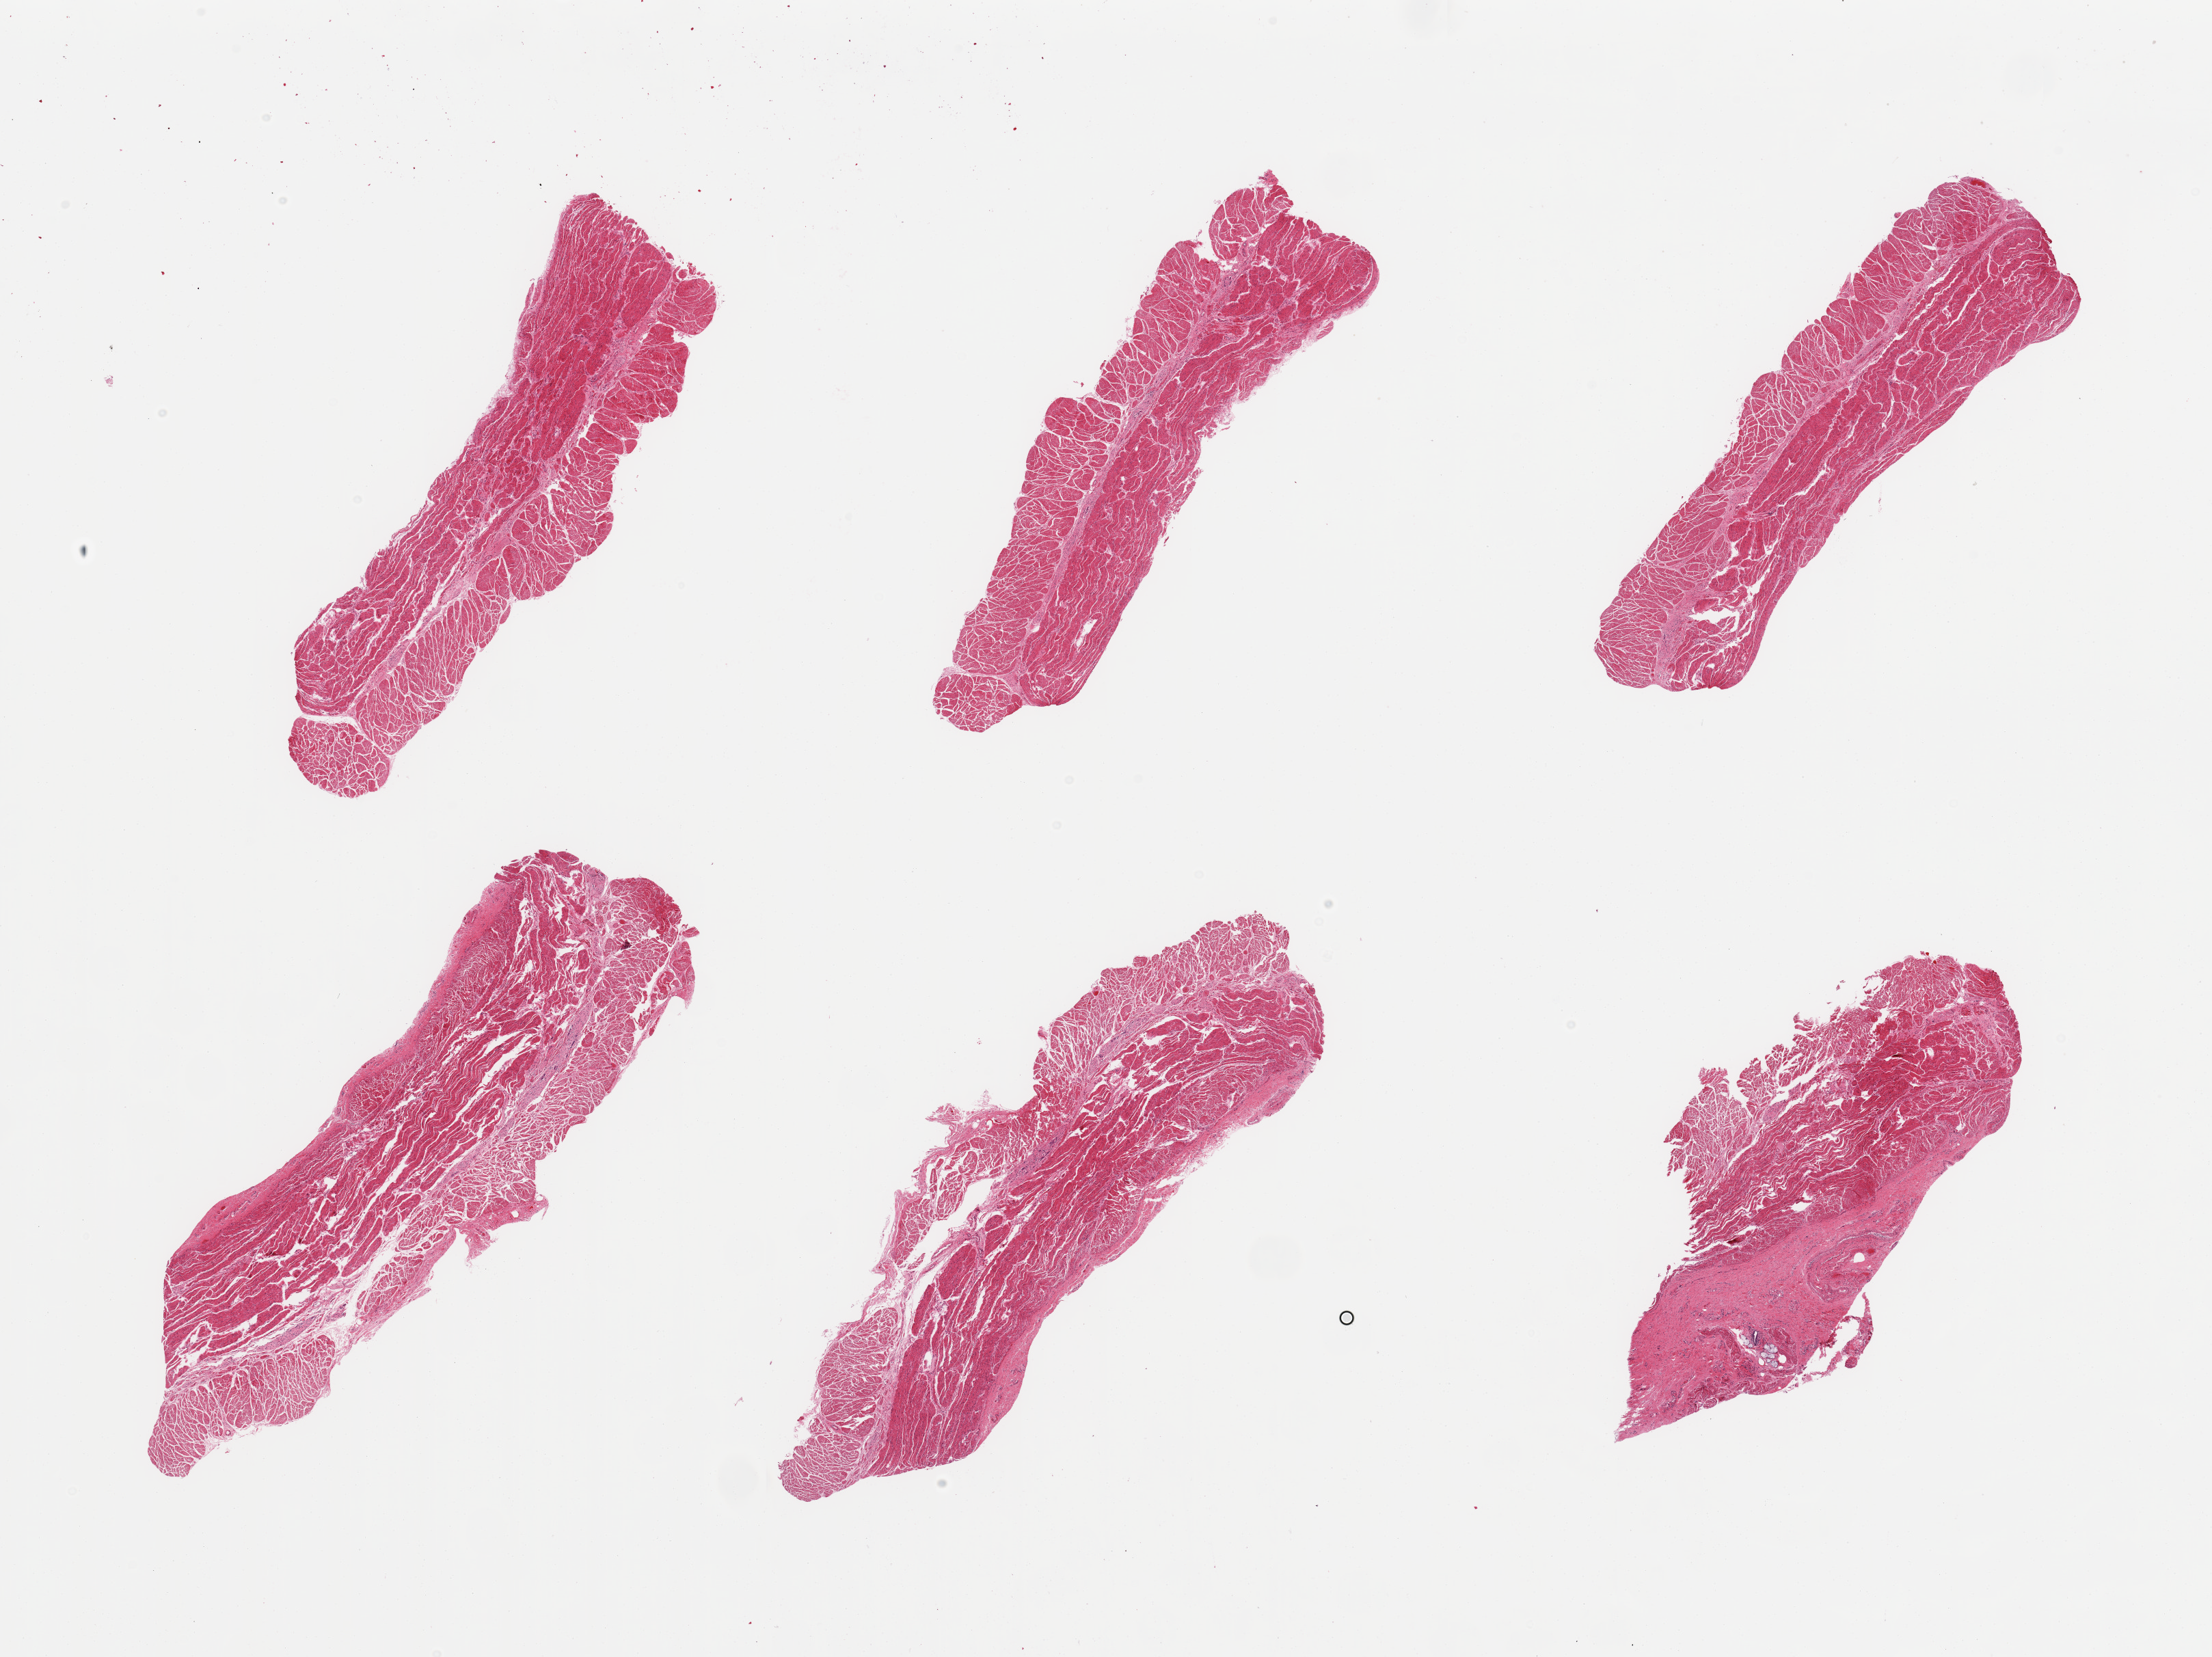
Hematoxylin and eosin (H&E) whole-slide image, brightfield — shown as a low-resolution overview of the whole scanned area (about 25.6 x 19.2 mm, slide scanned at 20x), PAXgene-fixed paraffin-embedded (PFPE) section, target tissue: esophageal muscle, tissue donor sample. Male donor.
Review note (as recorded): 6 pieces, confirmed target muscularis.